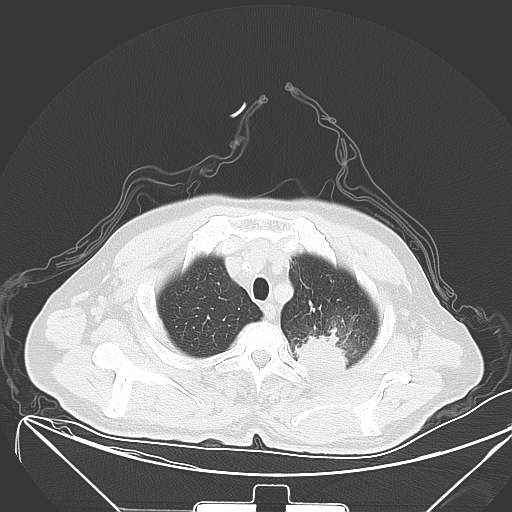
Chest CT, one axial slice. Position 51 of 64 along the scan axis. Lung window (W 1500 / L -600 HU). 512 × 512 image matrix, field of view 431 × 431 mm. Patient: male, 58 years. Case-level facts recorded for this patient, not image findings: clinical TNM (as recorded): T2b N3 M1b.
Outlined on this slice (bounding box drawn by a radiologist):
- lung tumour (recorded histology: adenocarcinoma): bounding box [x1, y1, x2, y2] px = [287, 324, 354, 377]